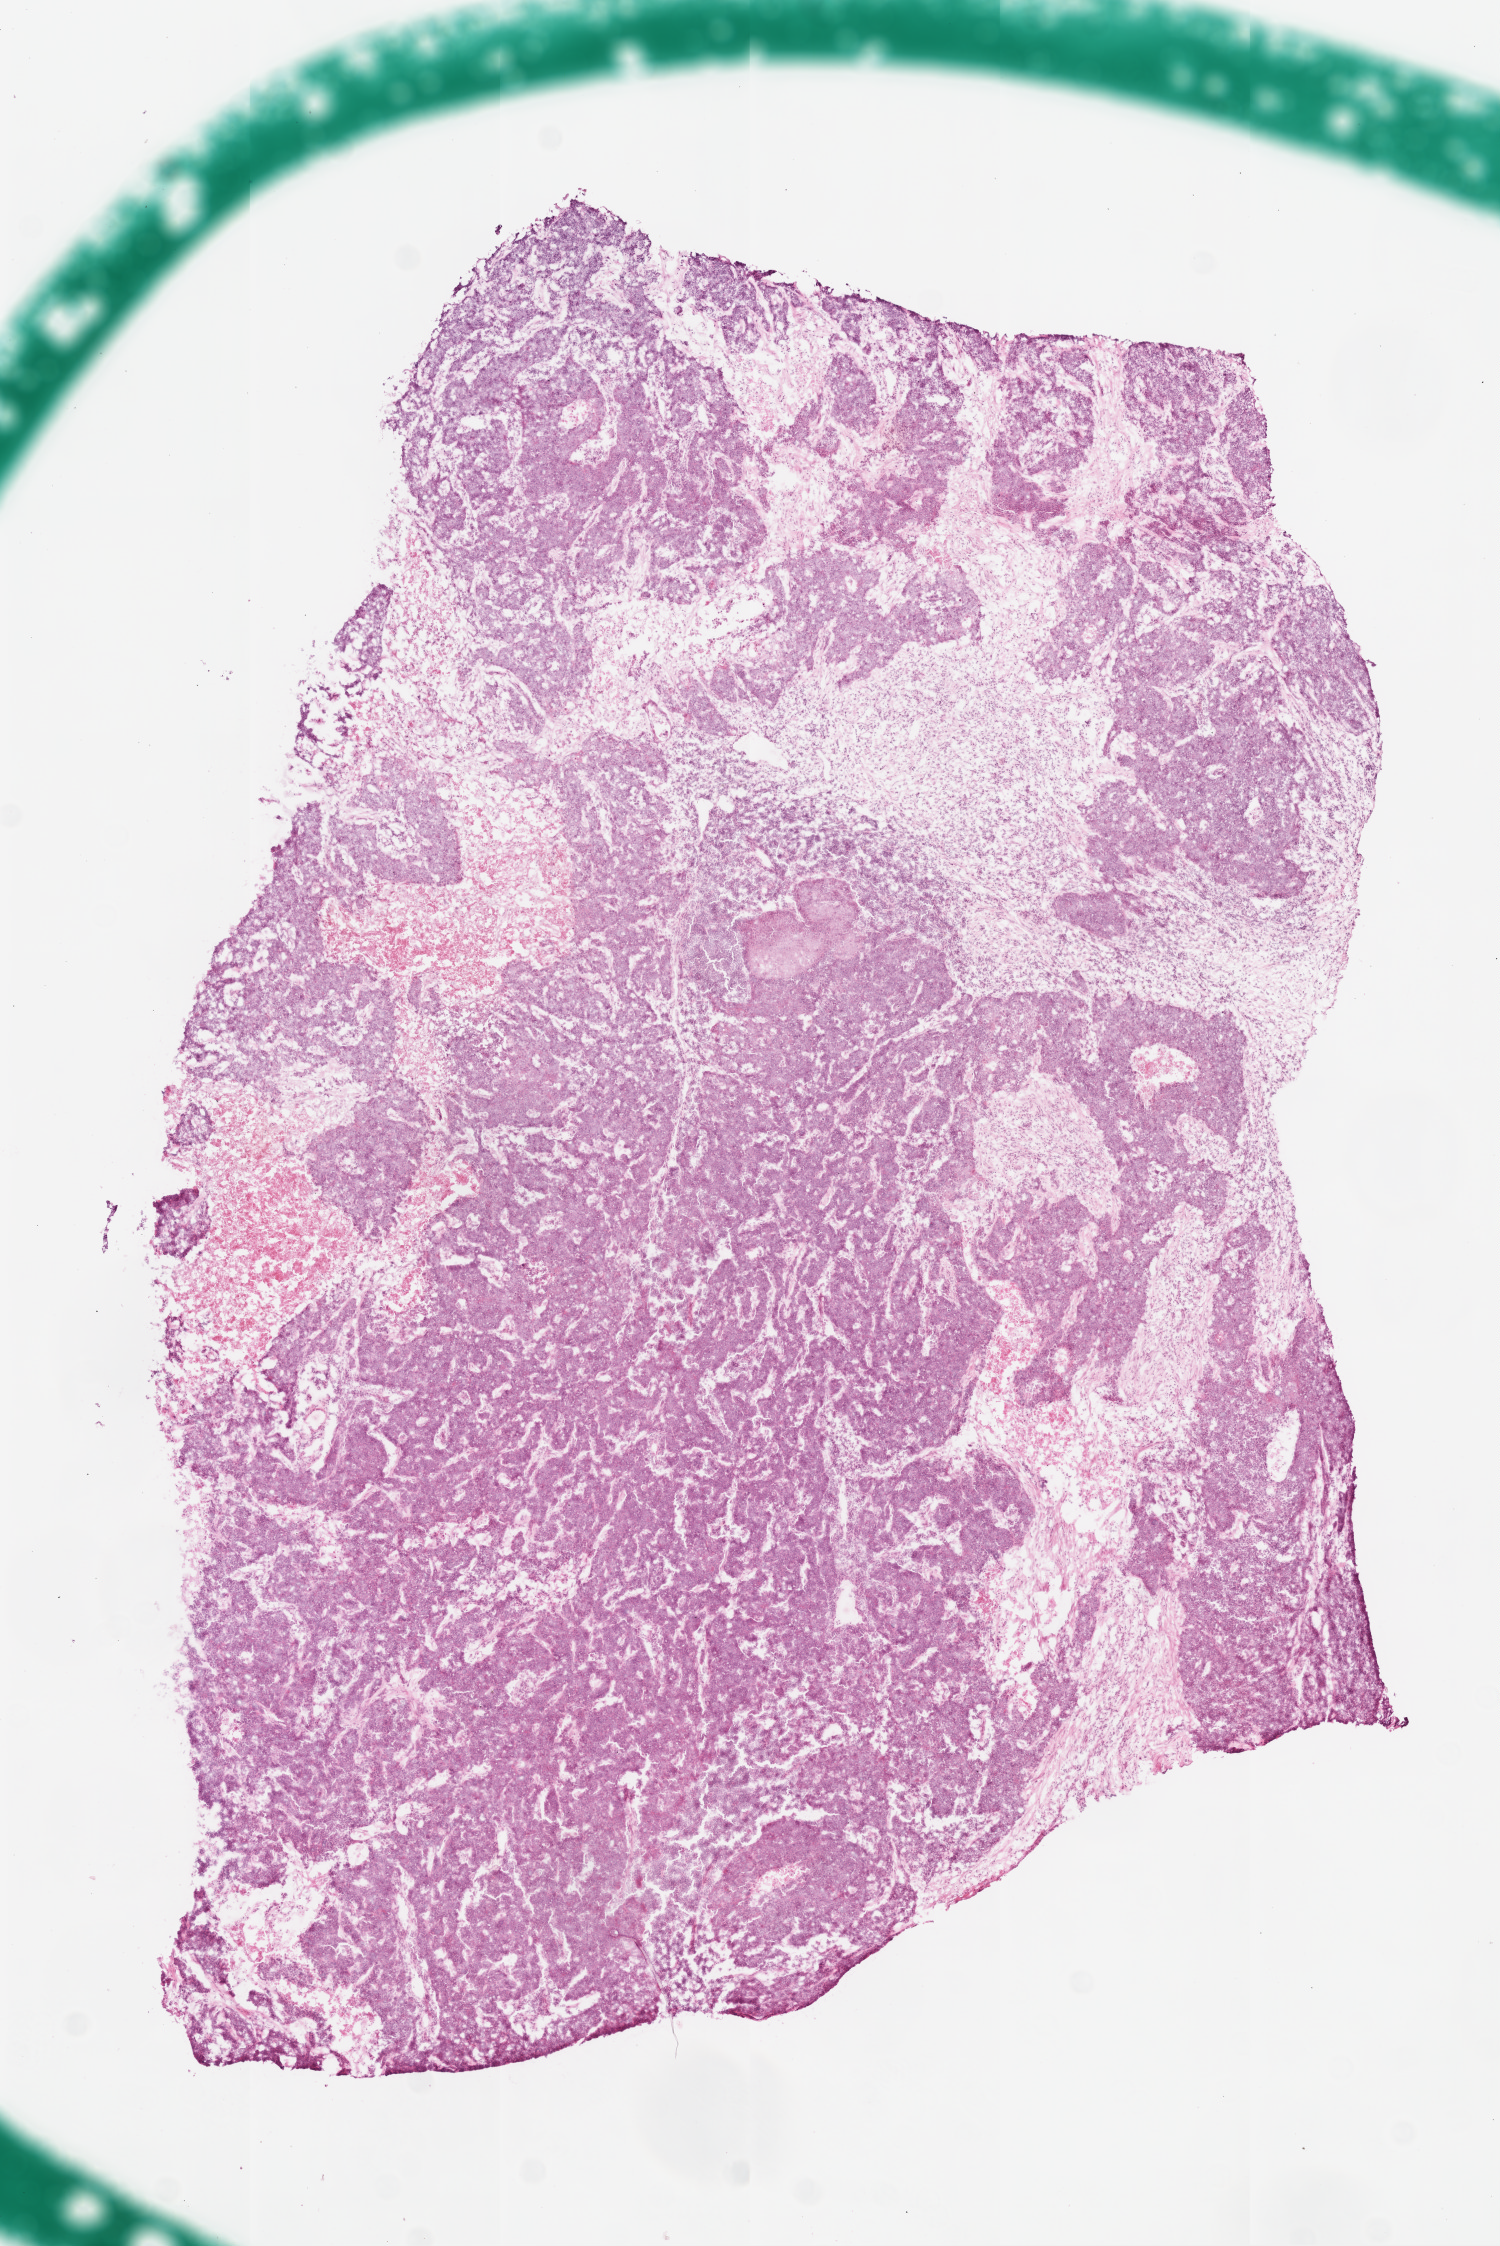
Hematoxylin and eosin (H&E) stained whole-slide image — whole scanned area (about 6.0 x 9.0 mm) shown as a low-resolution overview, frozen section from the top of the tissue portion, primary tumour sample from the head and neck. Patient: male, age at initial diagnosis 48 years. Composition of this section per pathologist review: tumour cells 91%, tumour nuclei 90%.
Pathologic diagnosis: Squamous cell carcinoma, NOS (tonsil, NOS).